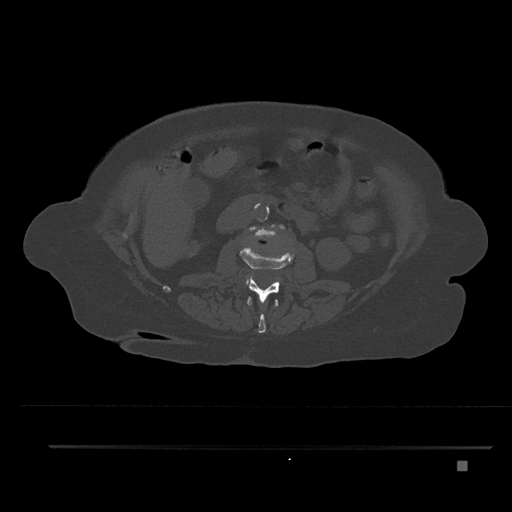
CT including the spine, one axial slice. Slice 170 of 797 in the series (ordered by position). Reconstruction kernel Br40s/3. Bone window (W 1800 / L 400 HU). 0.5 mm slice thickness. 512 × 512 image matrix. Patient: female, 76 years. From the clinical record (not read from this slice): primary cancer: lung; vertebrae with lytic lesions (as recorded): T11, L3.
Outlined on this slice (semi-automatically segmented with operator editing):
- L1 vertebra: box from (x=247, y=296) to (x=278, y=333) px
- L2 vertebra: (x=240, y=247)–(x=294, y=303)
- L3 vertebra: (x=246, y=225)–(x=285, y=282)